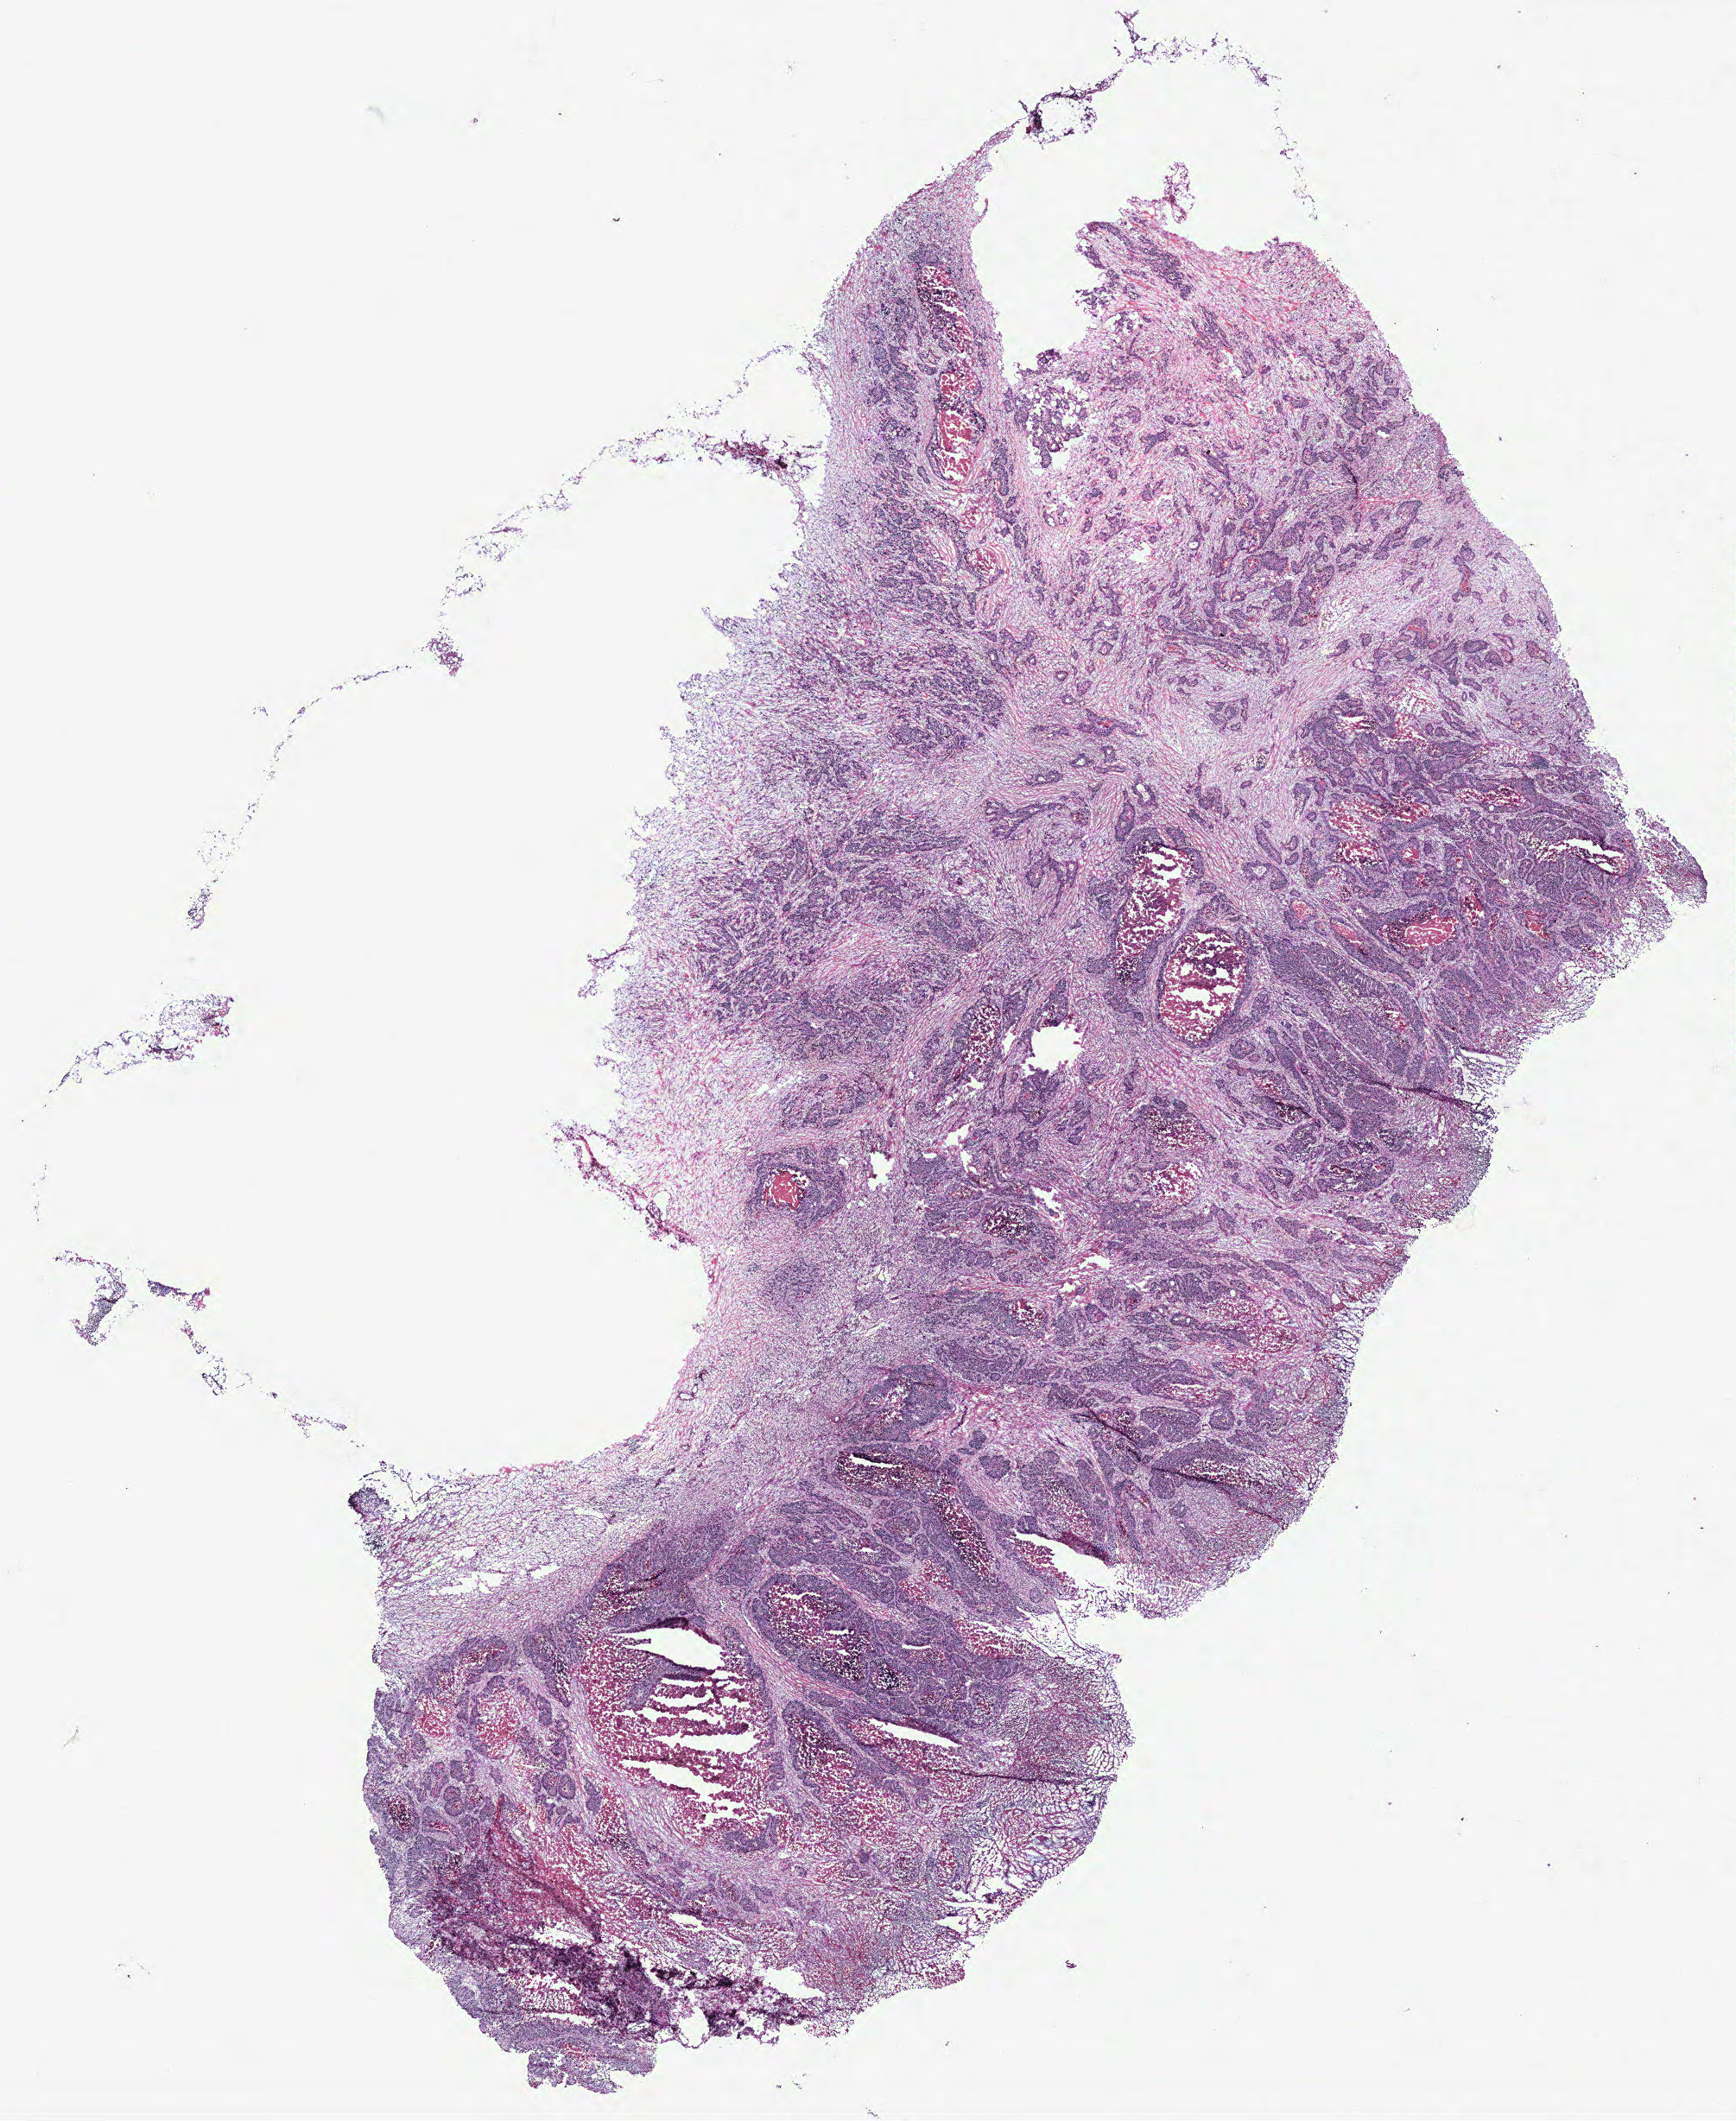
Digitized H&E tissue section (whole slide) — low-resolution overview of the scanned area, about 16.1 x 19.7 mm (from a 40x scan), tumour tissue sample, colon. Female, 74 y/o.
Diagnosis: Adenocarcinoma, NOS.